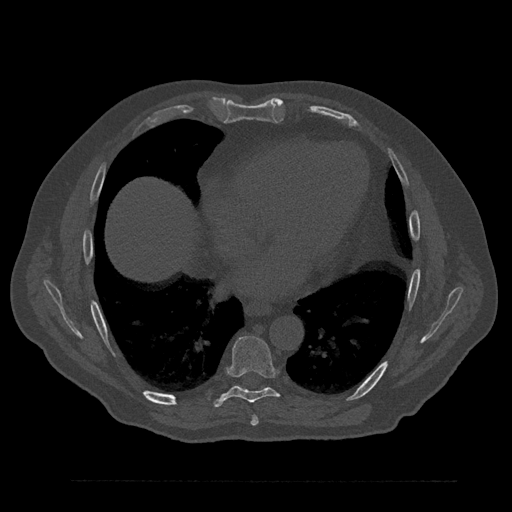
CT including the spine, one axial slice; slice 452 of 797 in the series (ordered by position); 120 kVp; bone window (W 1800 / L 400 HU); 0.5 mm slice thickness; 512 × 512 image matrix, field of view 430 × 430 mm. Patient: male, 61 years. Case-level facts recorded for this patient, not image findings: primary cancer: prostate.
Annotated regions visible in this slice (semi-automatic segmentation, software-assisted and operator-edited):
- T7 vertebra: bounding box <251,415,259,426> (left, top, right, bottom; pixels)
- T8 vertebra: <212,335,280,408>